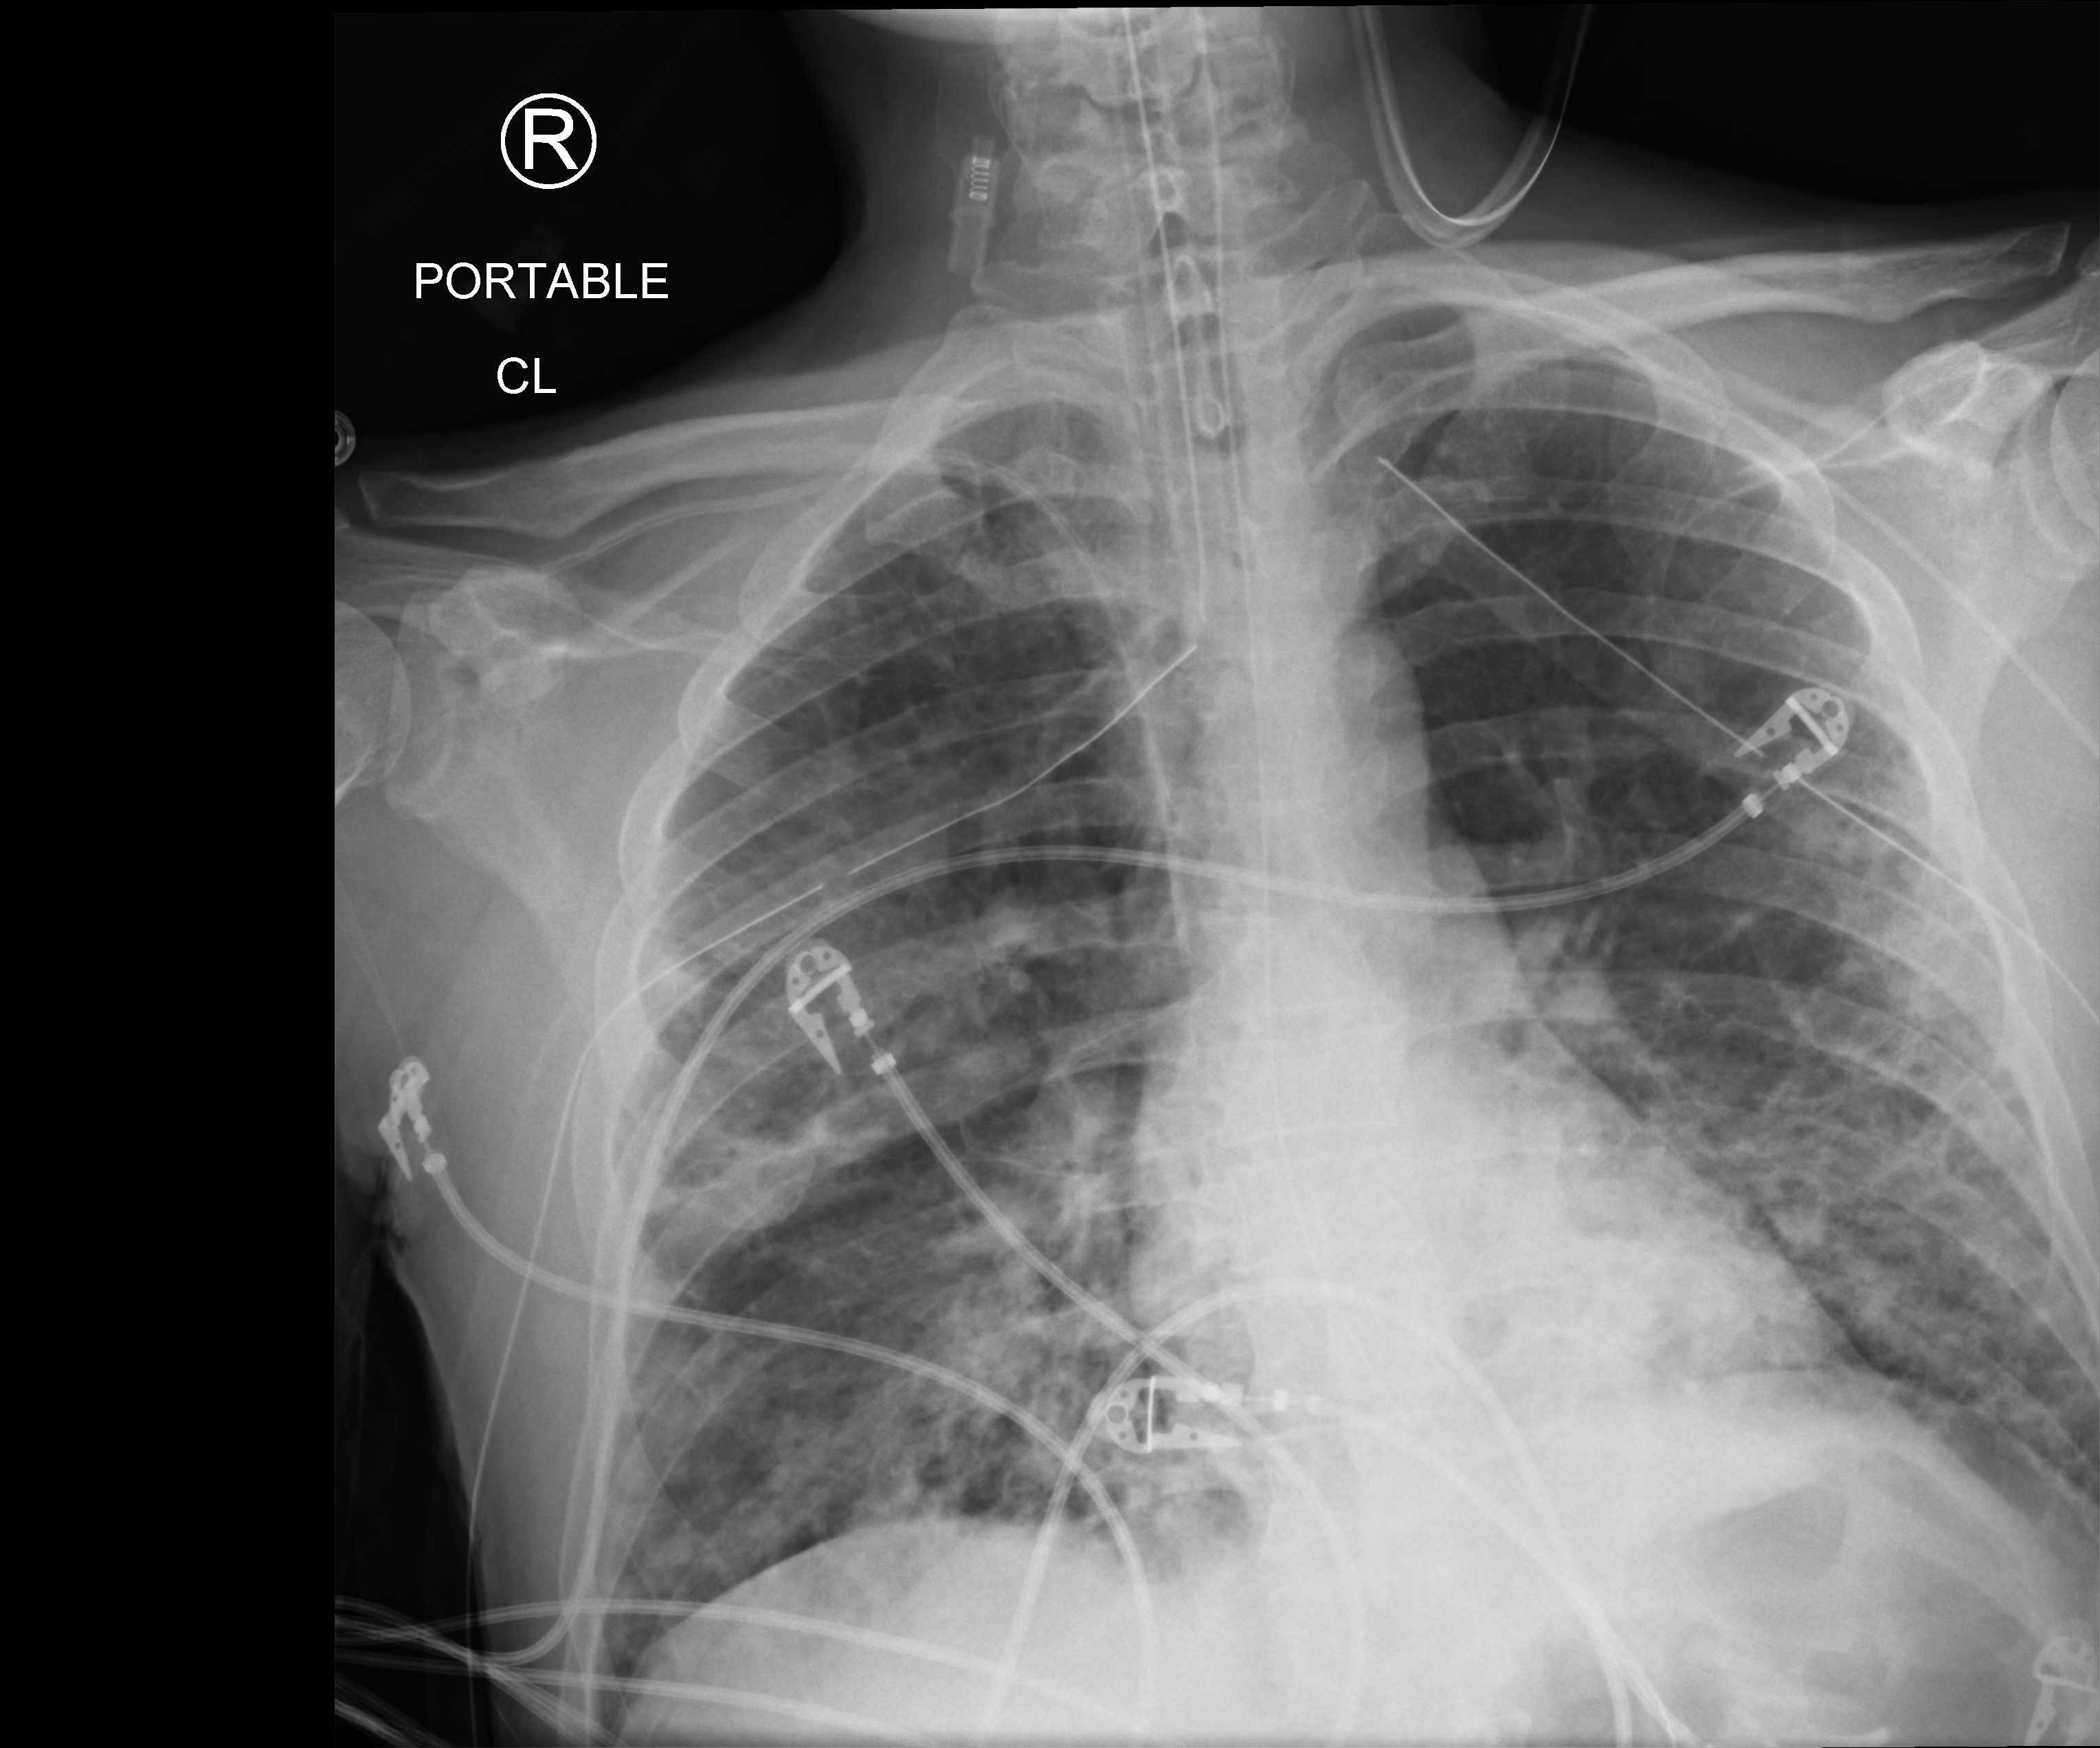
Chest X-ray (portable); anteroposterior (AP) projection. Male patient hospitalised with COVID-19, age 18–59 years.
Admission-level facts for this patient (not findings on this image; timing relative to this image not recorded):
- admitted to intensive care during this hospital stay: yes
- mechanically ventilated during this hospital stay: yes
- hypertension (admission record): yes